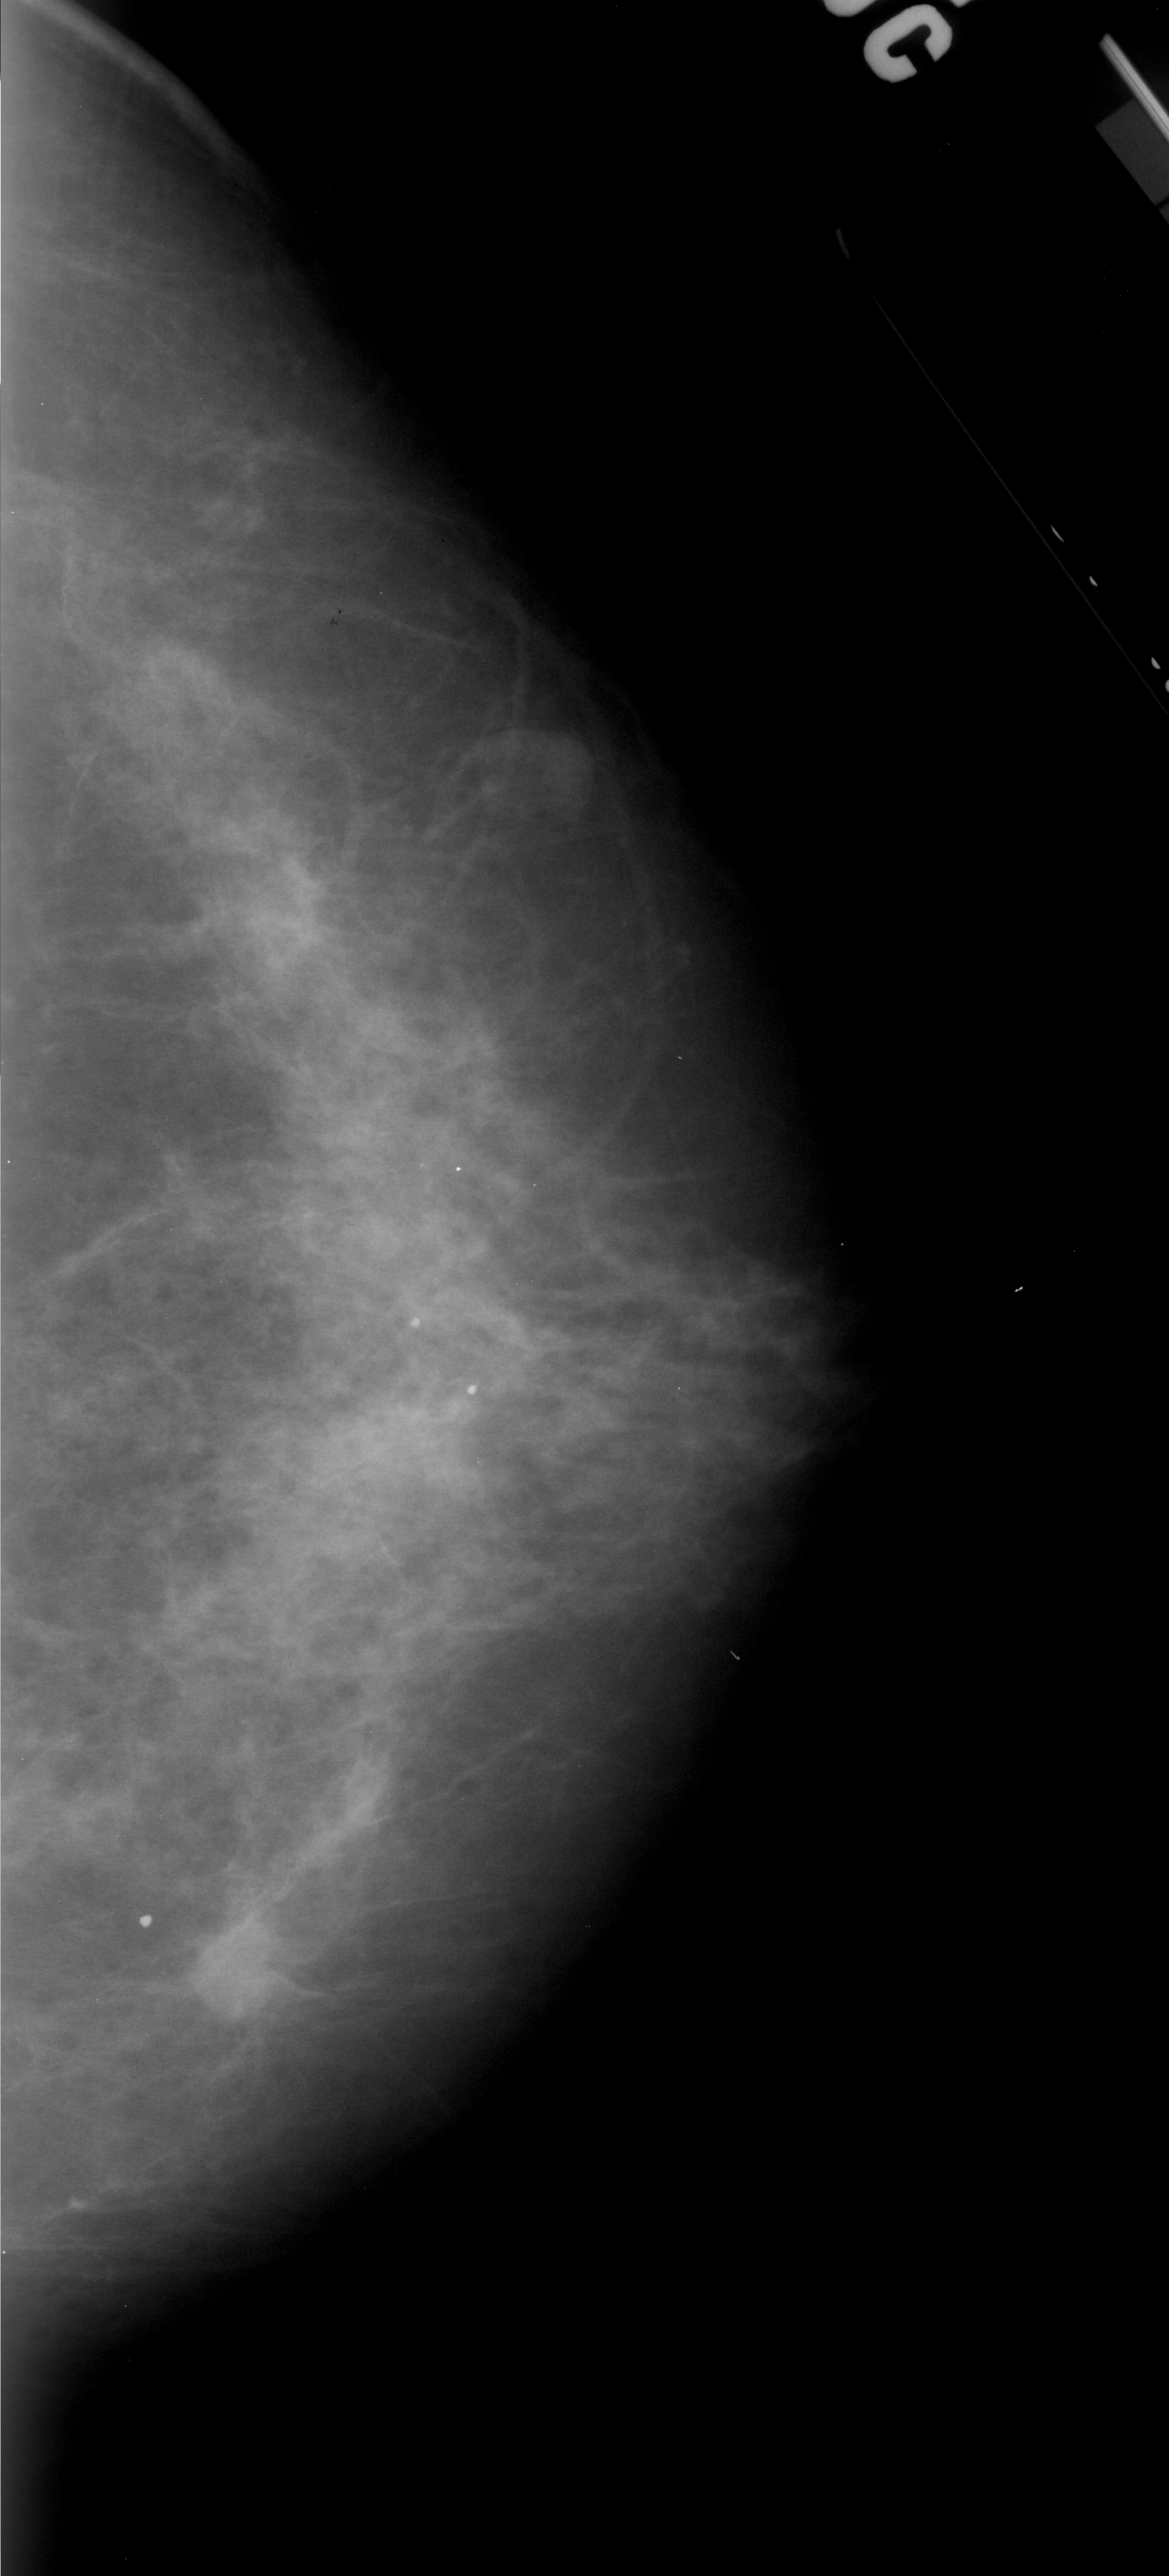
Digitized screen-film mammogram; right breast; CC view; BI-RADS breast density category 3 (scale 1–4).
- Abnormality record for this image: mass, shape lobulated, margins ill defined; BI-RADS assessment category 4; subtlety rating 4 on a 1 (subtle) to 5 (obvious) scale; pathology result (as recorded, not read from the image): malignant.